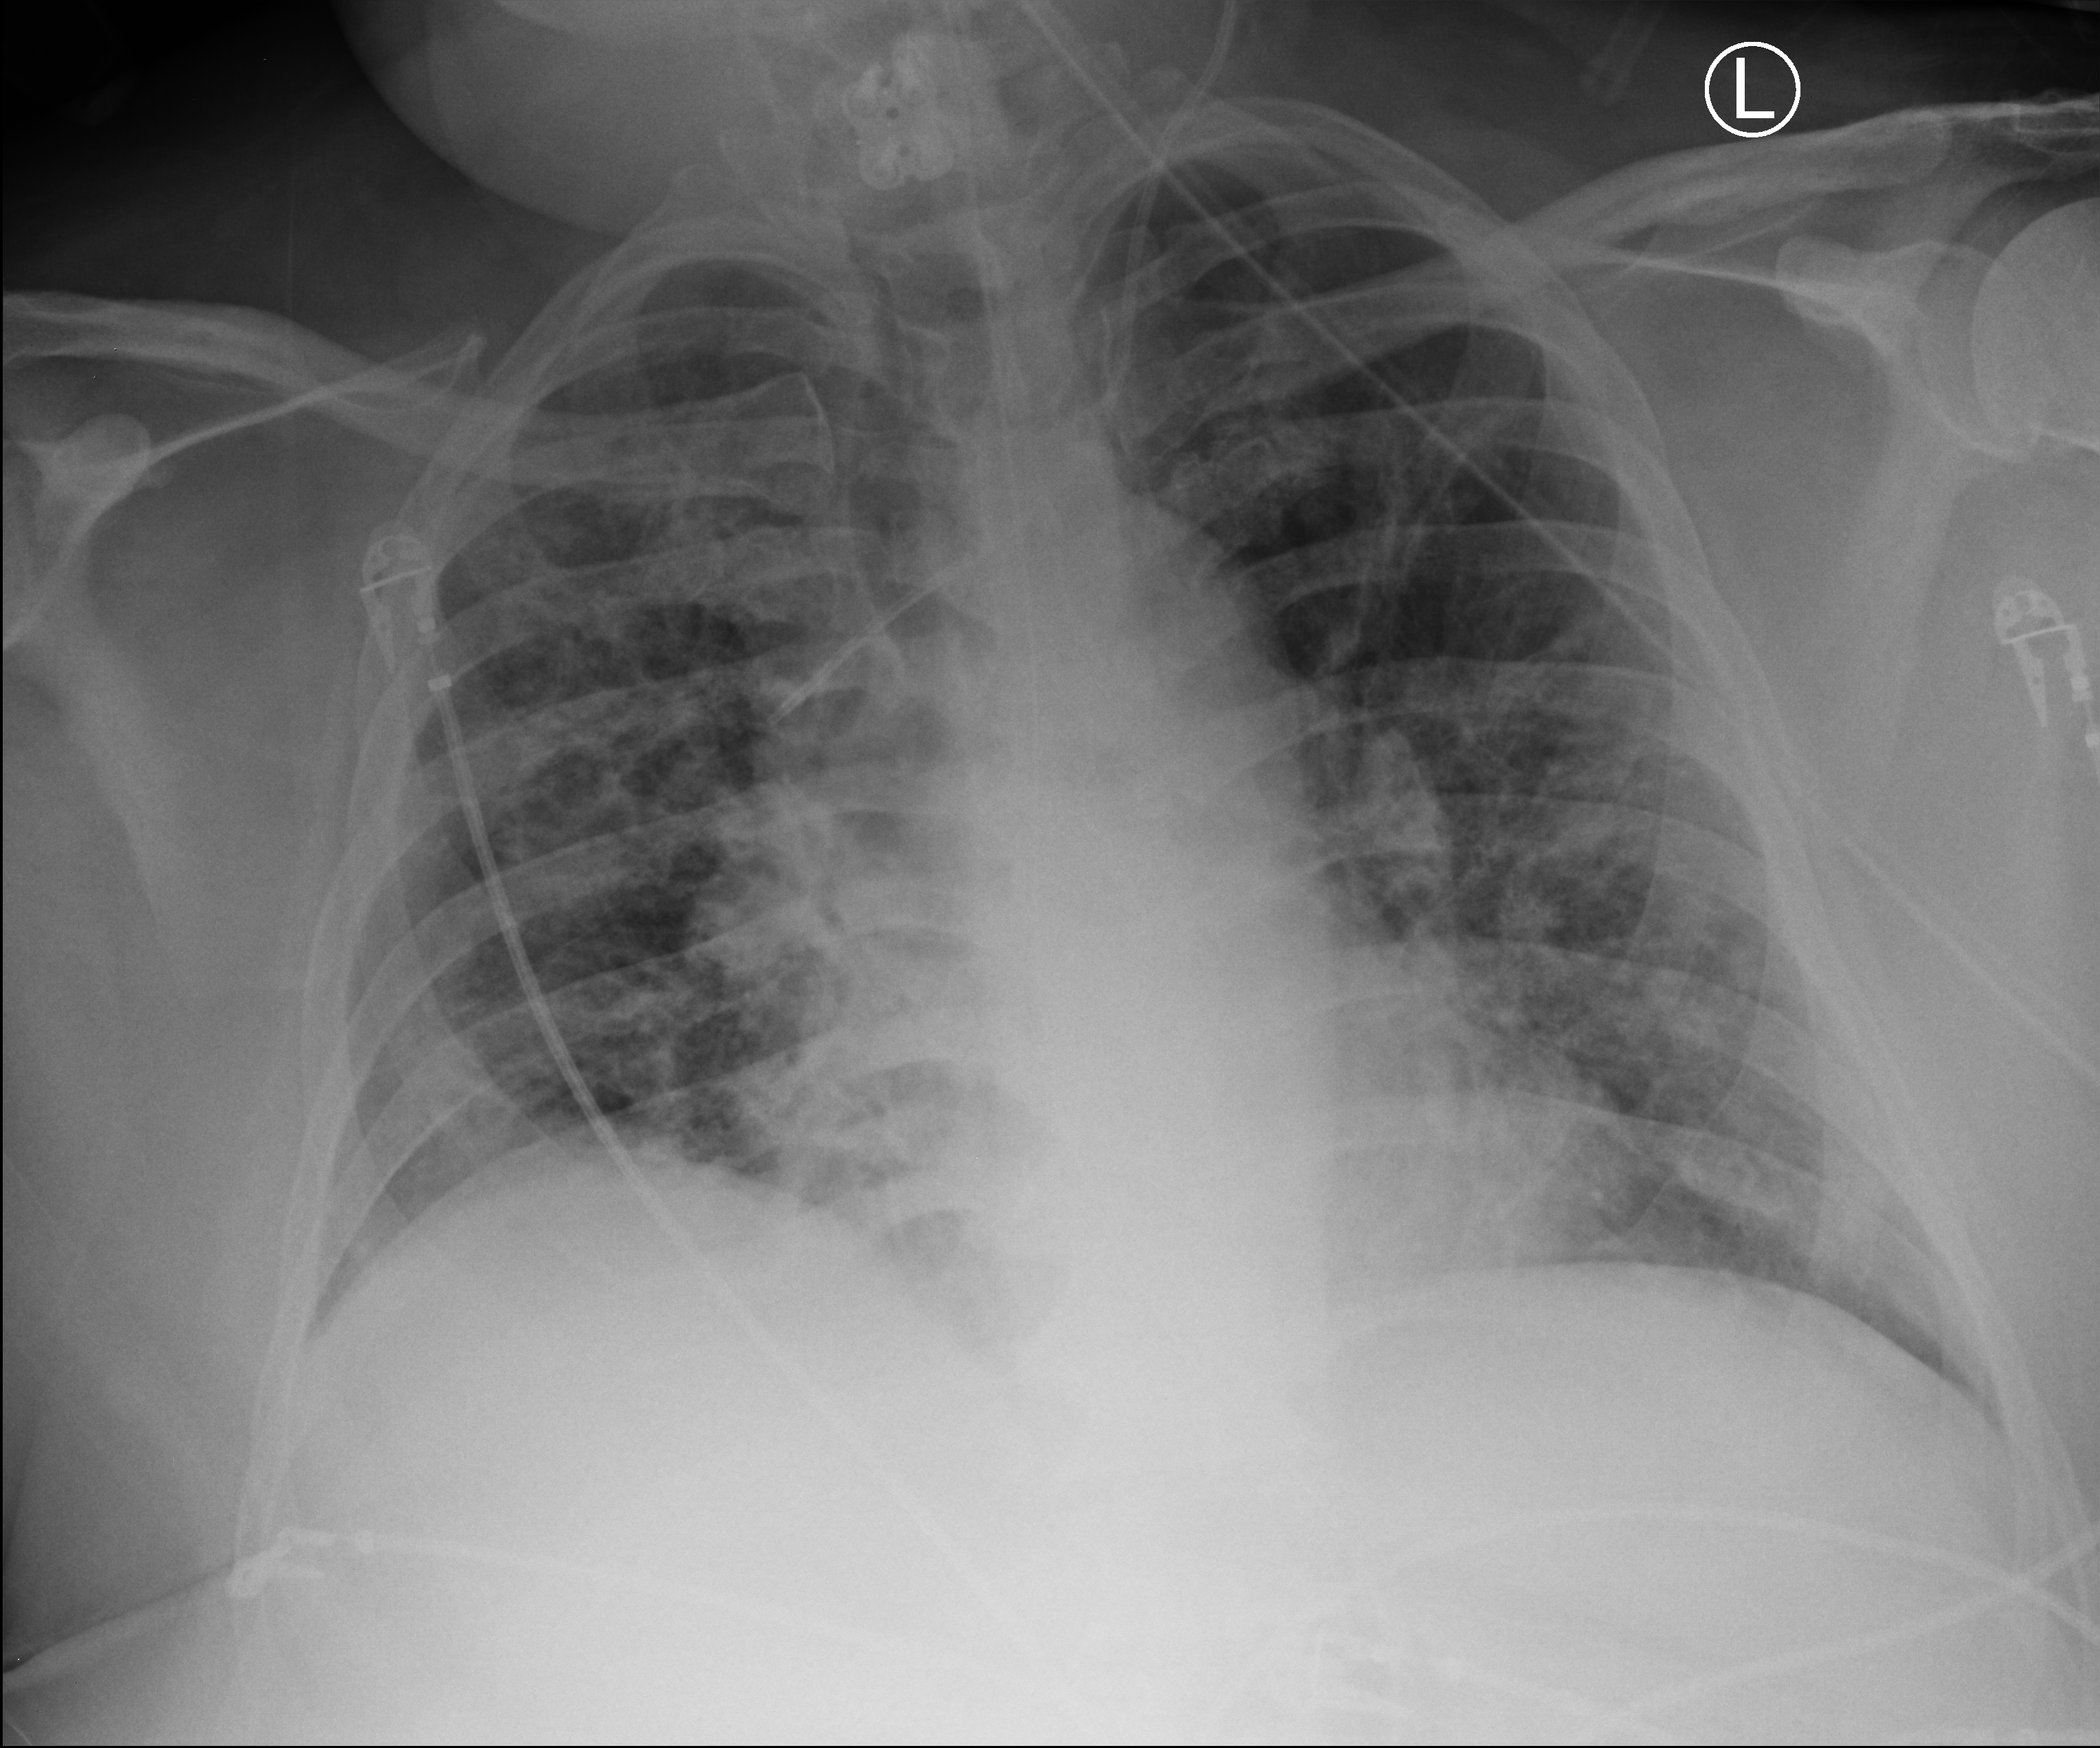
Chest X-ray (portable). Male patient hospitalised with COVID-19, age 18–59 years.
Admission-level facts for this patient (not findings on this image; timing relative to this image not recorded):
- diabetes (admission record): no